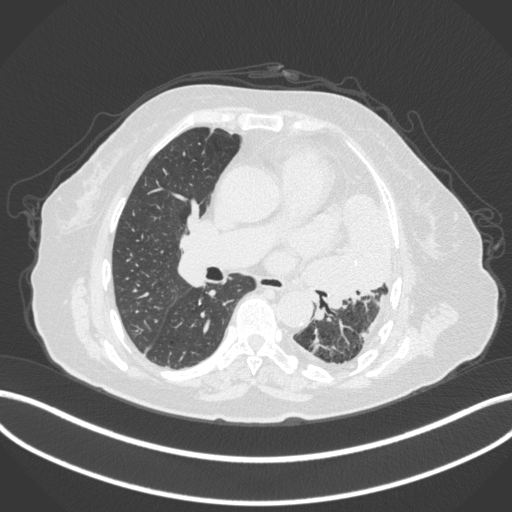
Chest CT, one axial slice; slice 199 of 399 in the series (ordered by position); reconstruction kernel B31f; lung window (W 1500 / L -600 HU); 512 × 512 image matrix, field of view 400 × 400 mm. Patient: female, 75 years. Case-level facts recorded for this patient, not image findings: clinical TNM (as recorded): T3 N3 M1.
Structures marked on this image (bounding box drawn by a radiologist):
- lung tumour (recorded histology: adenocarcinoma): bounding box (x1, y1, x2, y2) in pixels: (317, 190, 393, 311)